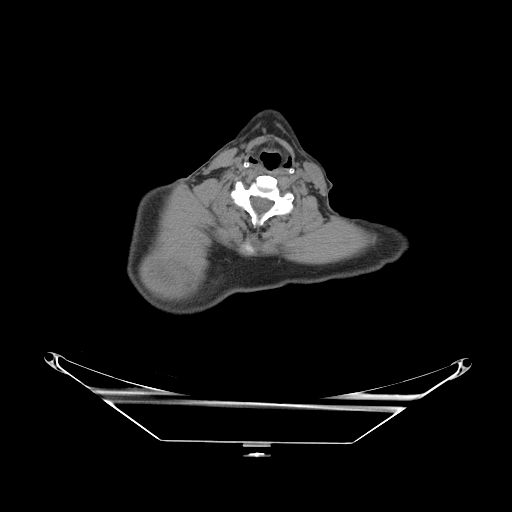
CT of an extremity soft-tissue mass (from a PET/CT study), one axial slice. Slice 220 of 267 in the series (ordered by position). Soft-tissue window (W 400 / L 40 HU). 3.75 mm slice thickness. 512 × 512 image matrix, field of view 500 × 500 mm. Male patient. Case-level facts recorded for this patient, not image findings: histological type: pleiomorphic spindle cell undifferentiated; grade: high; site of the primary tumour: right parascapusular.
Outlined on this slice (expert contour drawn on MRI and transferred to this co-registered scan by the dataset authors):
- gross tumour volume including surrounding oedema: box from (x=142, y=265) to (x=202, y=300) px
- gross tumour volume (mass): (x=144, y=265)–(x=177, y=296)